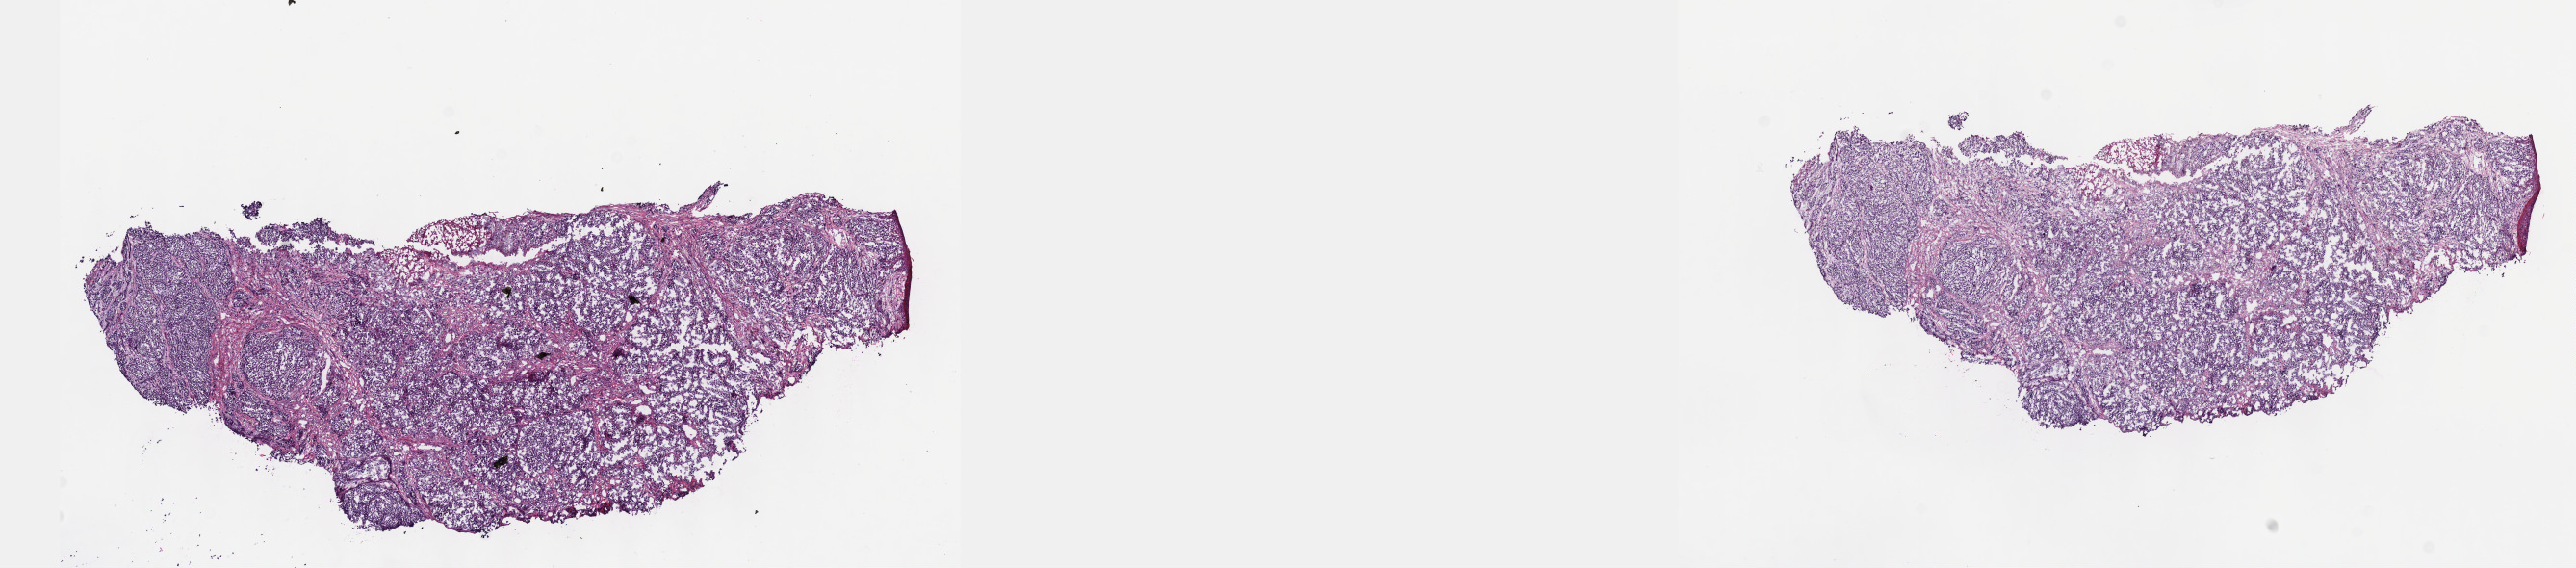
Hematoxylin and eosin (H&E) stained whole-slide image, shown as a low-resolution overview of the whole scanned area (about 21.6 x 4.8 mm). Frozen section from the top of the tissue portion. Sample: primary tumour, skin. Female, age 62 years at initial diagnosis. Composition of this section per pathologist review: tumour cells 100%, tumour nuclei 75%.
Pathologic diagnosis: Malignant melanoma, NOS.